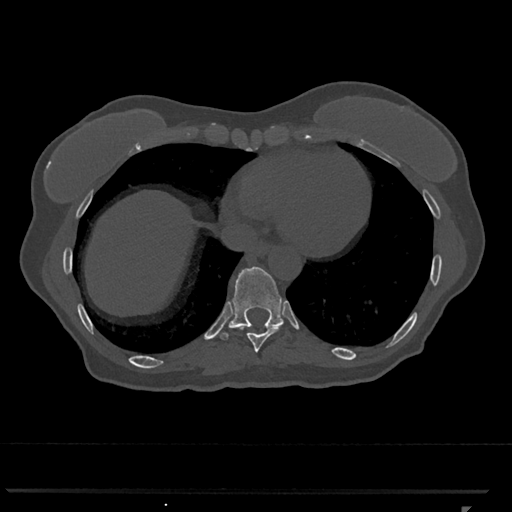
CT including the spine, one axial slice; slice 592 of 793 in the series (ordered by position); reconstruction kernel Br40s/3; bone window (W 1800 / L 400 HU); 512 × 512 image matrix, field of view 380 × 380 mm. Patient: female, 62 years. Case-level facts recorded for this patient, not image findings: primary cancer: renal.
Structures marked on this image (semi-automatic segmentation, software-assisted and operator-edited):
- T10 vertebra: bounding box [x1, y1, x2, y2] px = [220, 266, 284, 339]
- T9 vertebra: [238, 325, 282, 352]